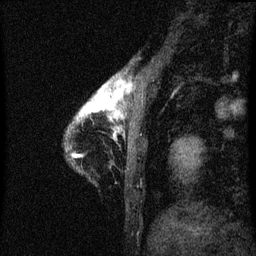
Breast MRI (dynamic contrast-enhanced), one sagittal slice; position 7 of 60 along the scan axis; dynamic contrast-enhanced series, image 2 of 3 at this slice position (ordered by acquisition); 1.5 T; TE 4.2 ms, TR 8 ms; 2 mm slice thickness; 256 × 256 image matrix, field of view 180 × 180 mm. Female patient, age 38 years.
Annotated regions visible in this slice (semi-automatically segmented with operator editing):
- analysis volume of interest (the breast-tissue region the enhancement analysis was run in; not a lesion): bounding box [x1, y1, x2, y2] px = [69, 80, 129, 145]
- tumour enhancement mask (voxels above the 70 % enhancement threshold inside the analysis volume of interest): [80, 80, 126, 119]